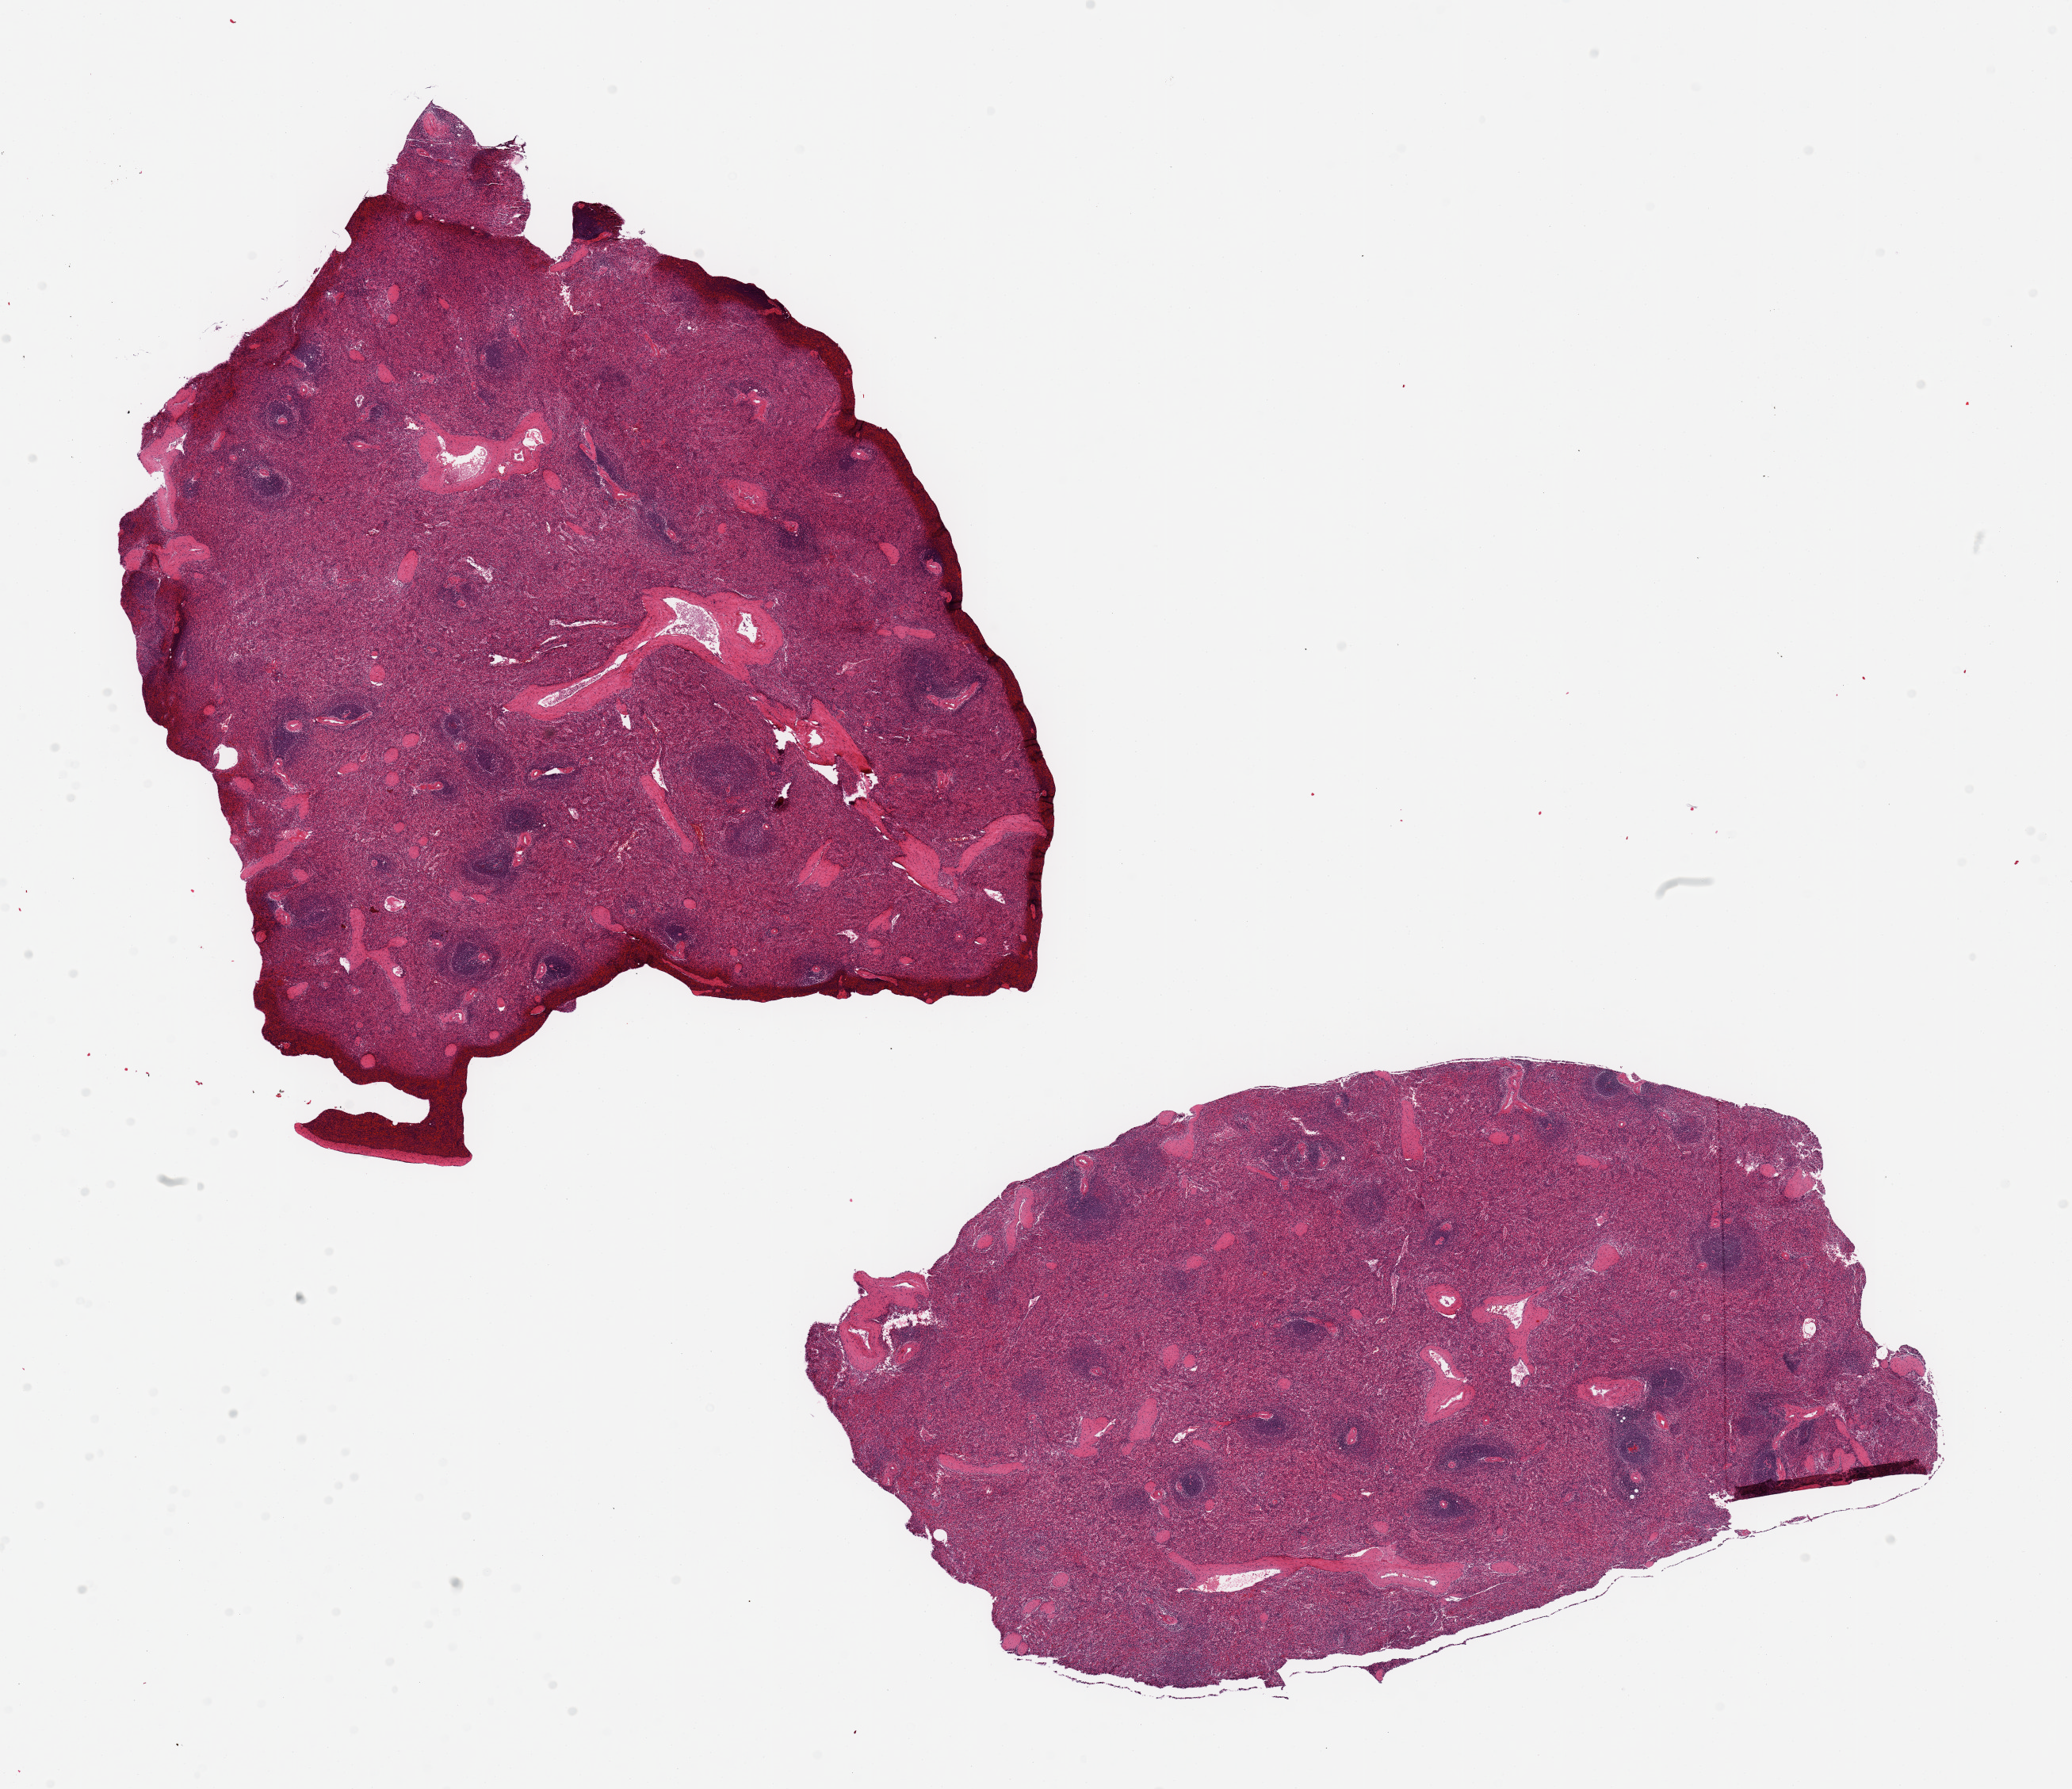
Whole-slide image, H&E stain, brightfield — a low-resolution overview of the entire scanned area, about 20.7 x 17.8 mm (slide scanned at 20x); PAXgene-fixed, paraffin-embedded tissue; sampled site (target tissue): spleen; donor tissue sample. Donor sex: female.
* reviewer comment on this tissue sample: 2 pieces, no abnormalities